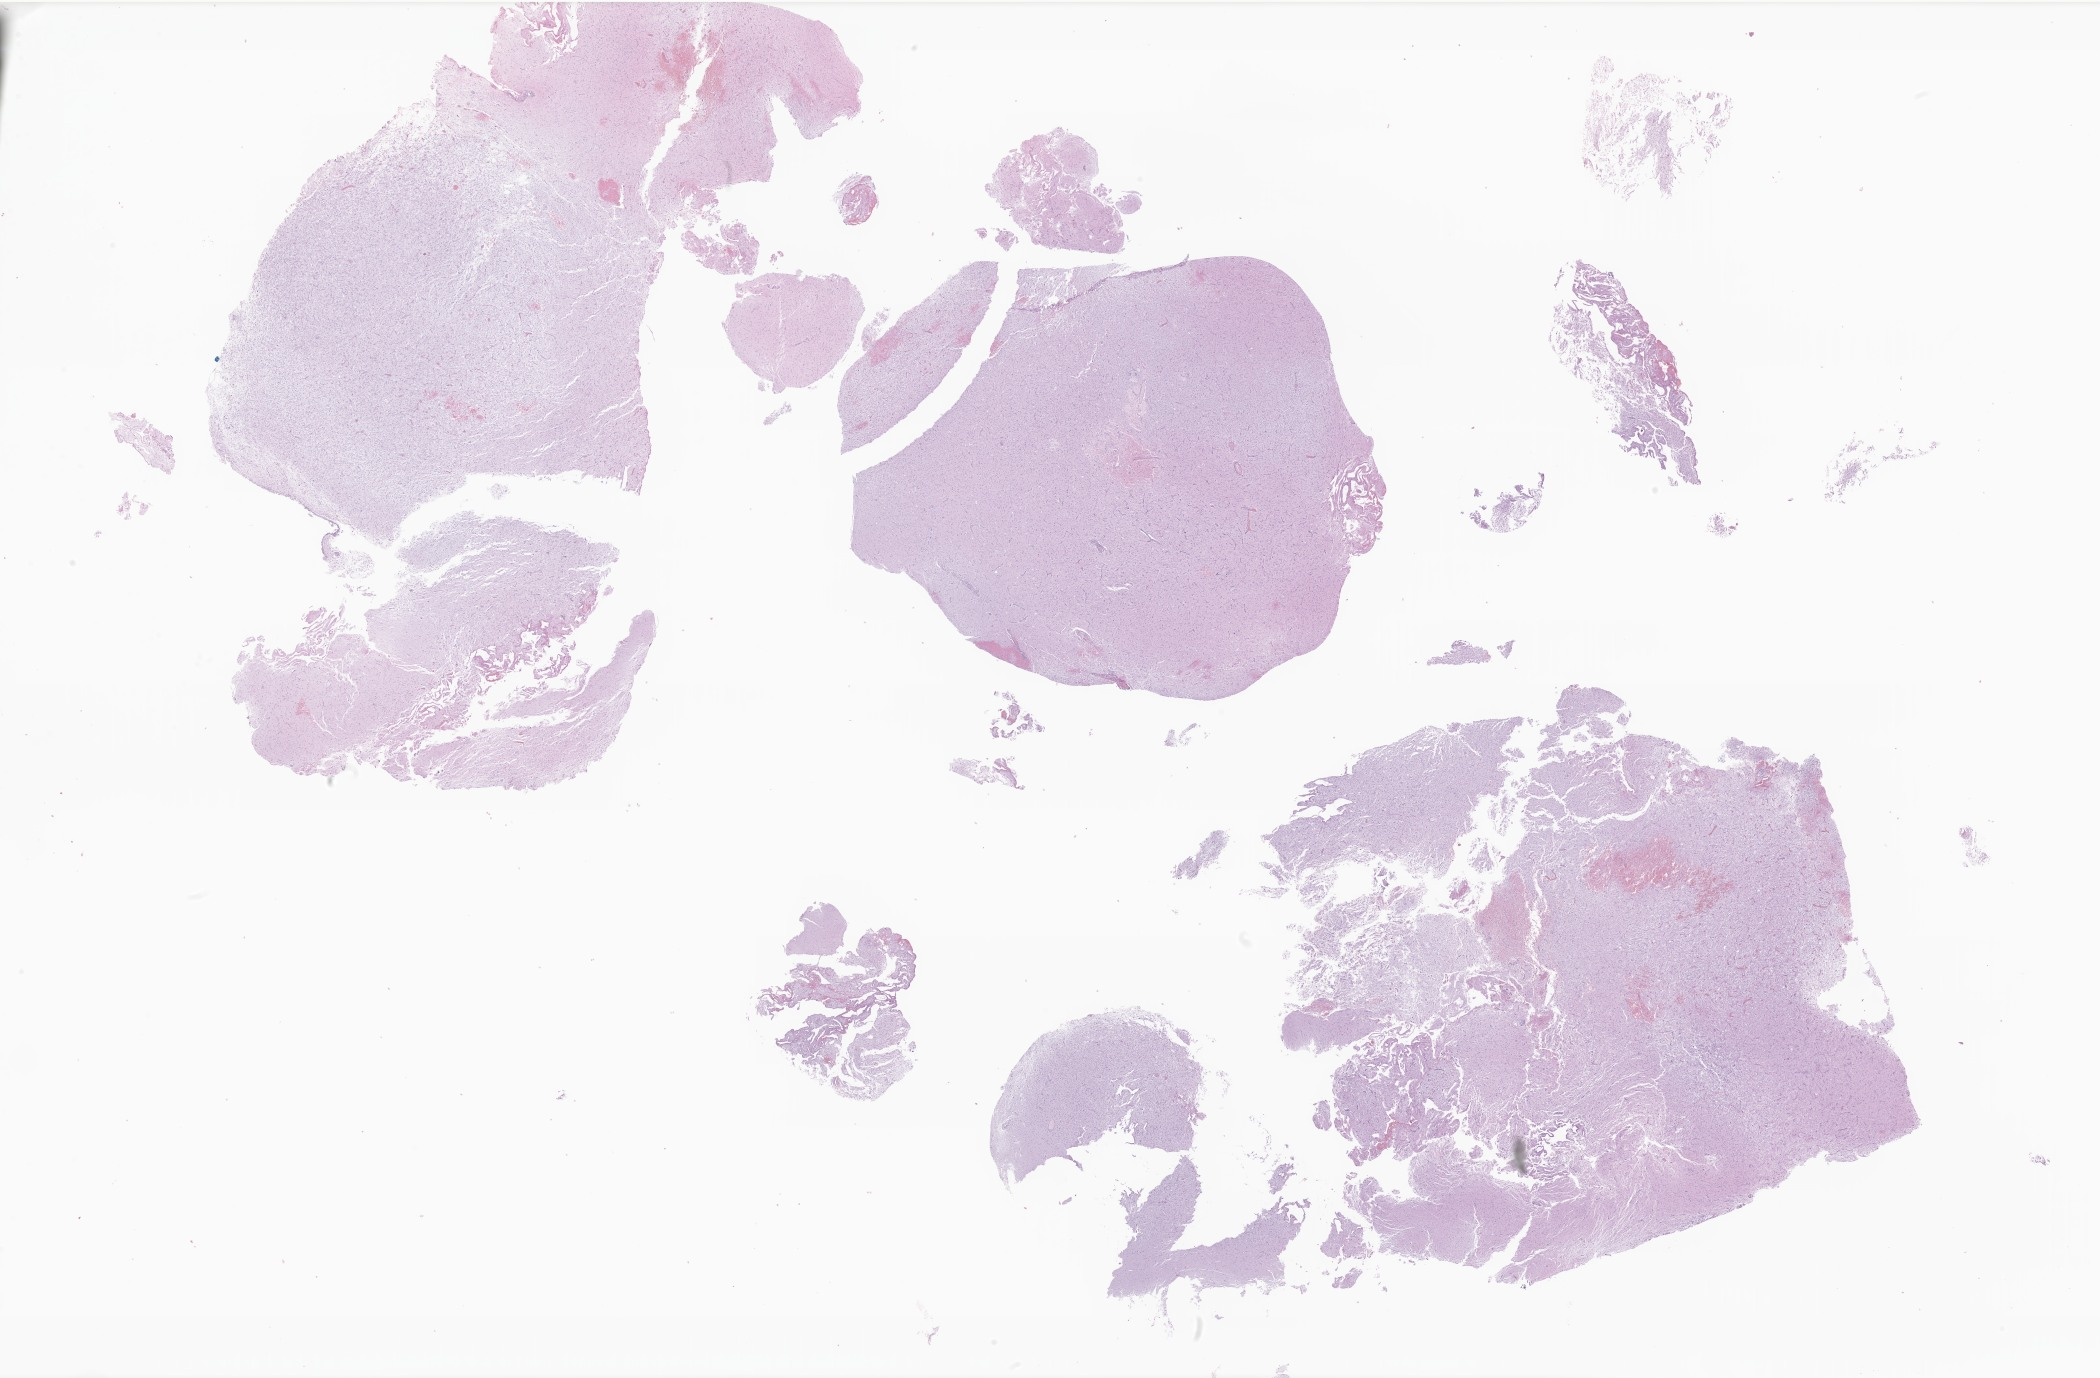
Hematoxylin and eosin (H&E) whole-slide image of tumor tissue from the brain, shown as a low-resolution overview of the whole scanned area (about 35.4 x 23.2 mm); formalin-fixed paraffin-embedded section. Patient female; age 222 months.
Recorded diagnosis: Neoplasm, uncertain whether benign or malignant.